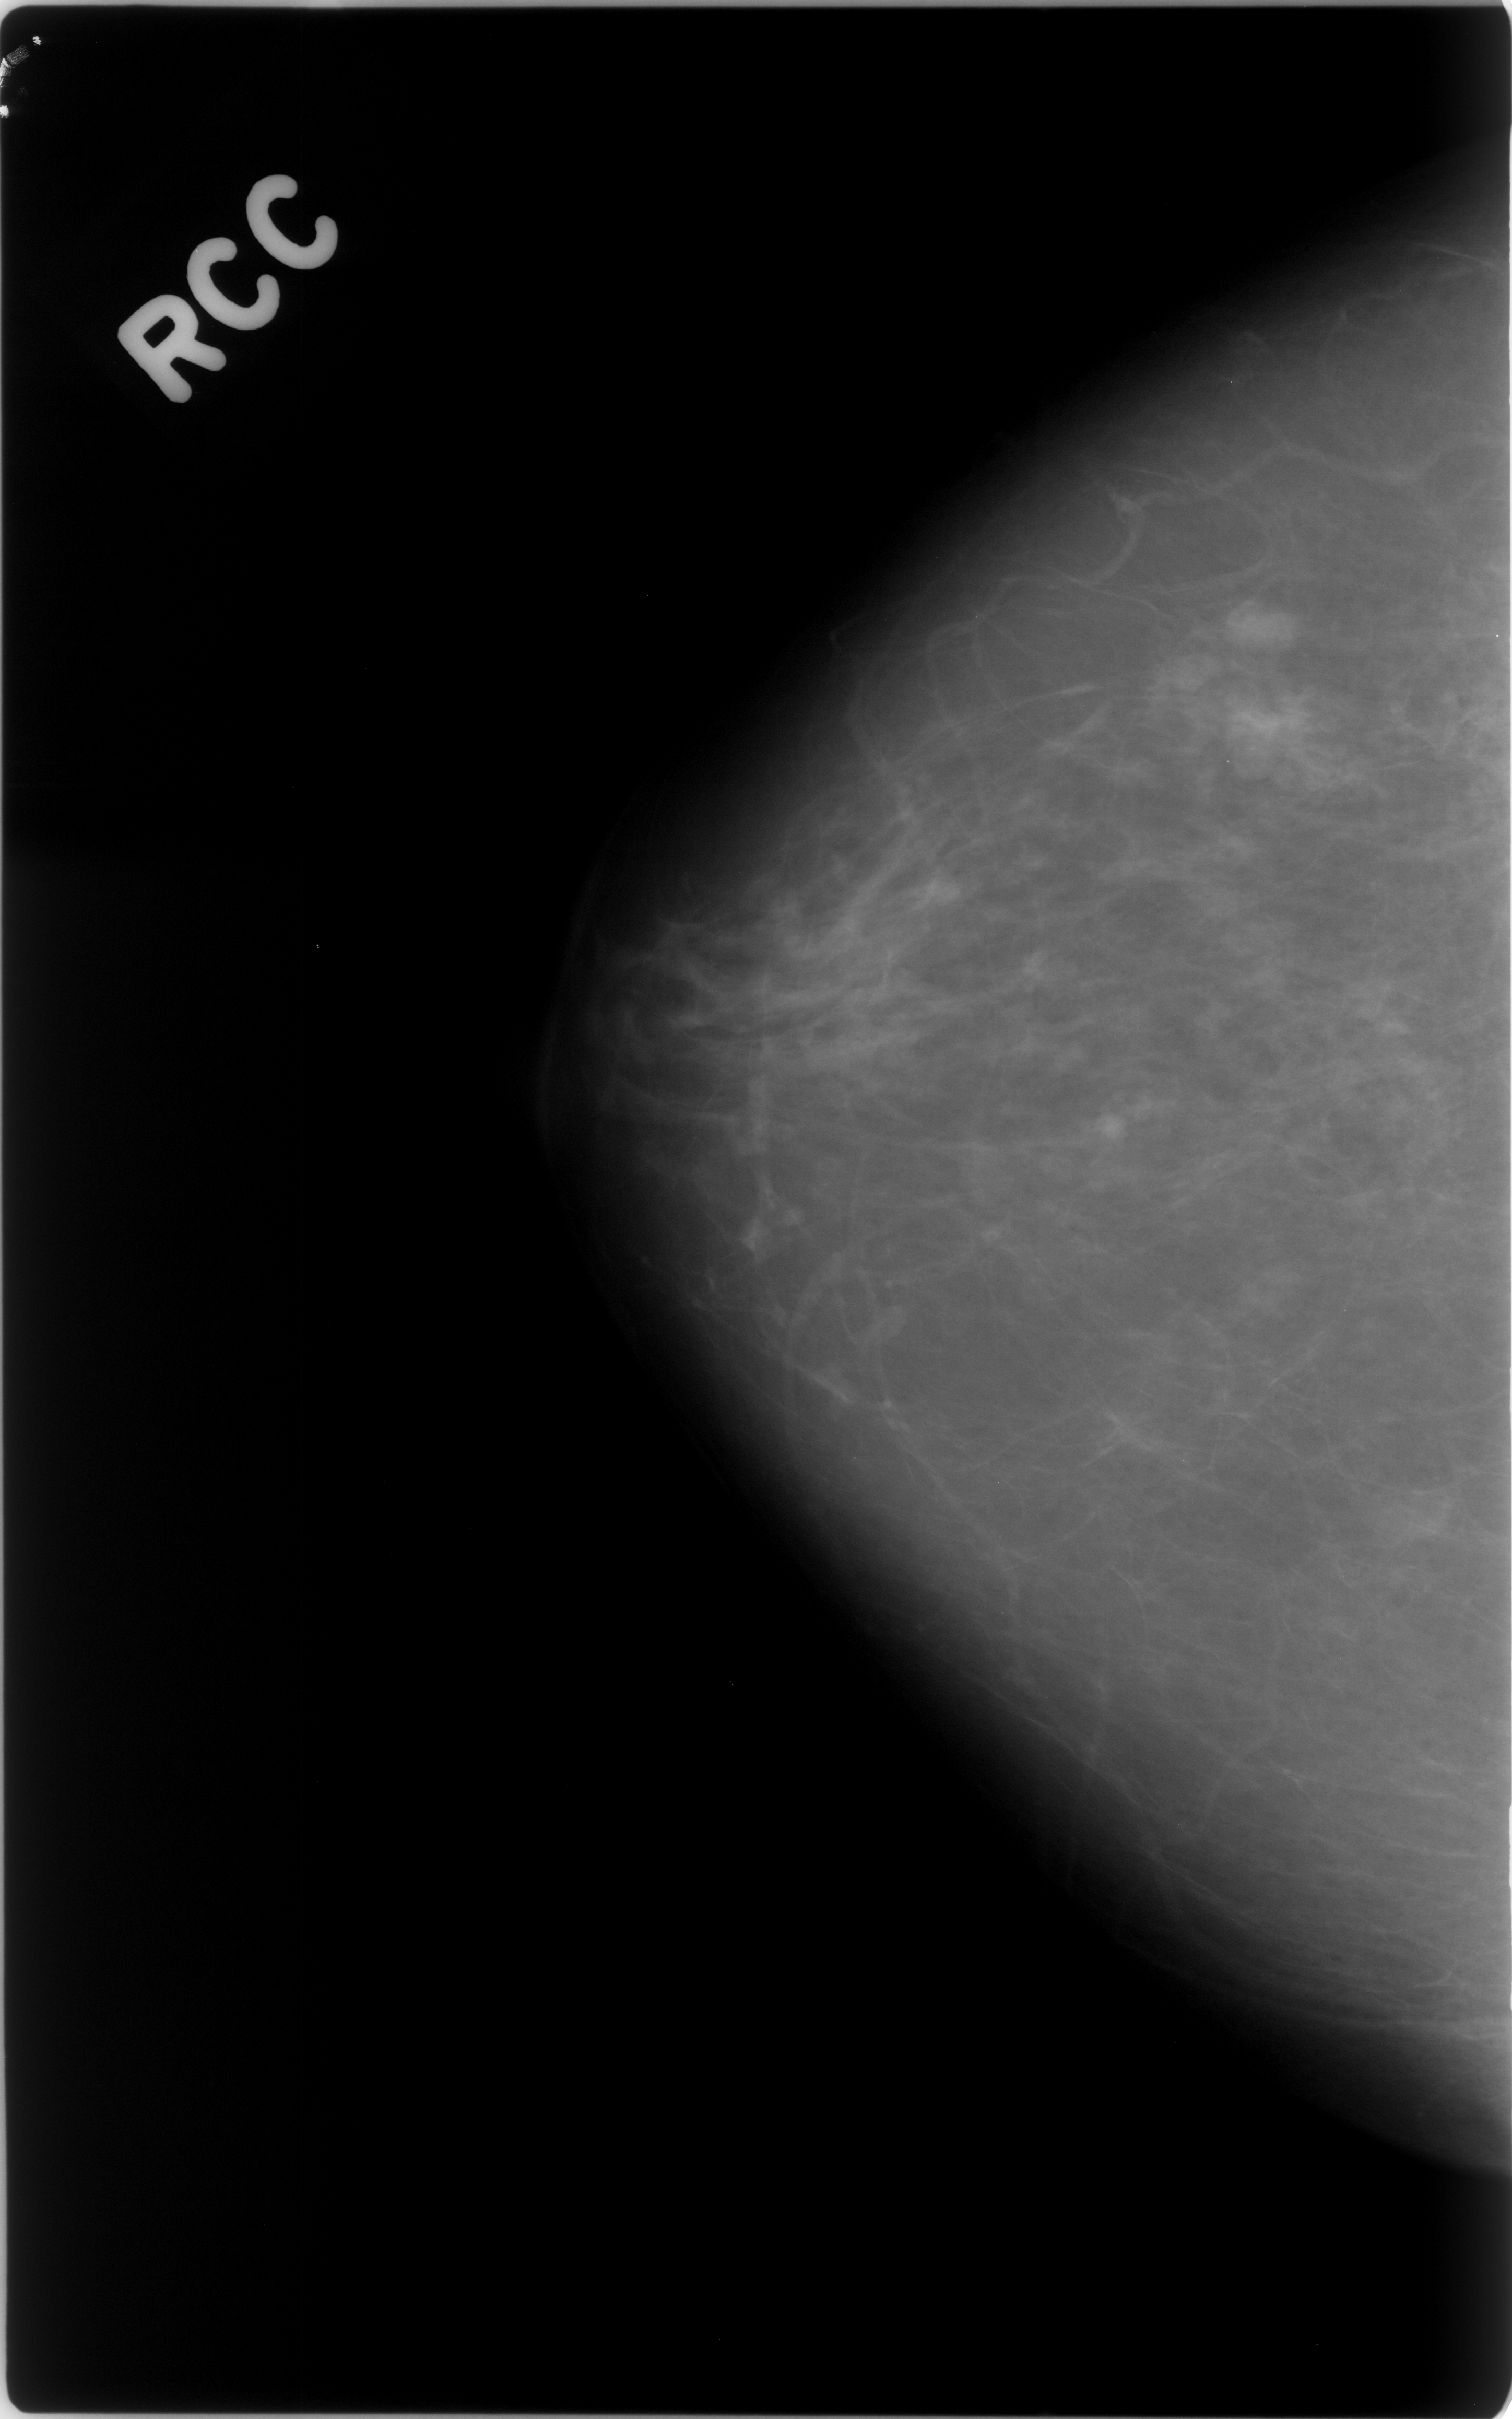
Mammogram (digitized film); right breast; craniocaudal (CC) view; breast composition: almost entirely fatty (BI-RADS density category 1 of 4); 1512 × 2419 image matrix.
Expert-marked regions of interest on this image (one box per marked abnormality):
- mass, shape lobulated, margins circumscribed; BI-RADS assessment category 3; subtlety rating 5 on a 1 (subtle) to 5 (obvious) scale; benign; no additional work-up was recommended (outcome (as recorded, no biopsy): benign without callback): bounding box <1195,649,1337,790> (left, top, right, bottom; pixels)